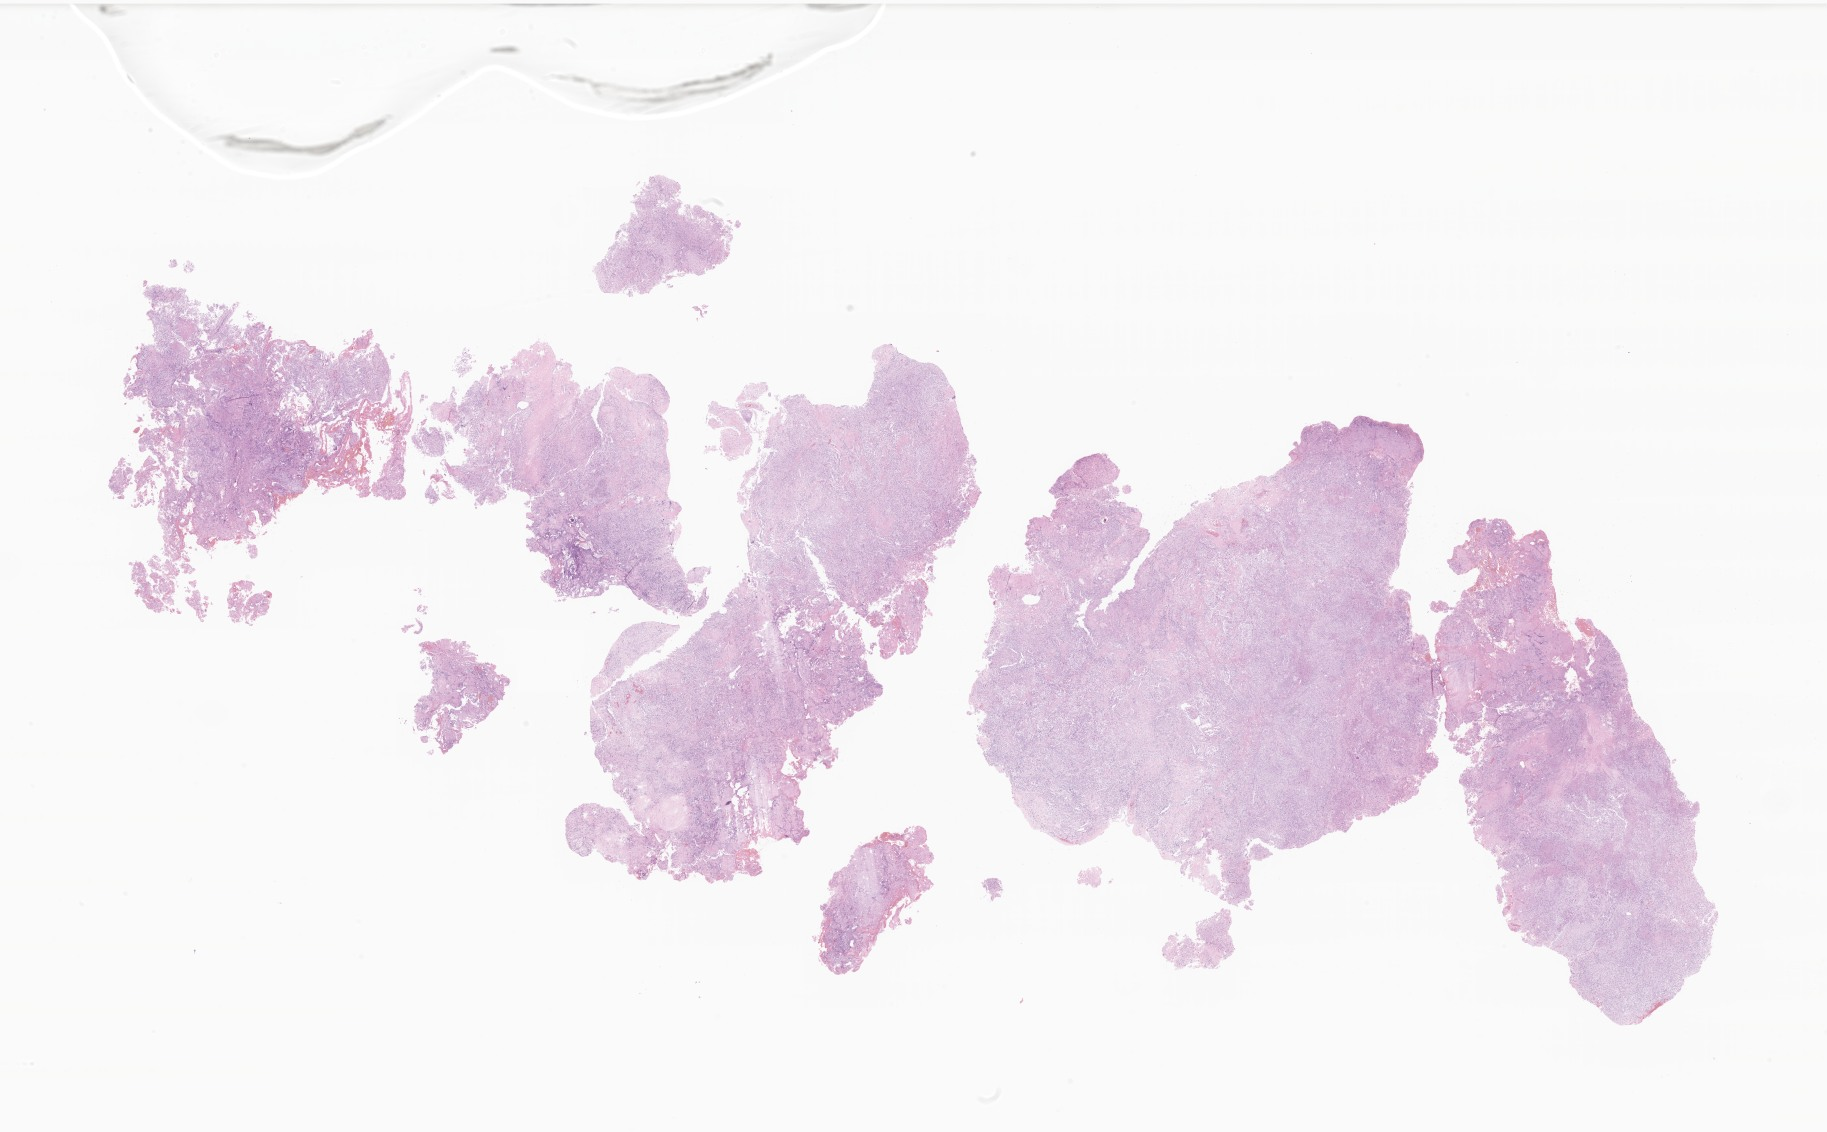
Whole-slide image, hematoxylin and eosin (H&E) stain of tumor tissue from the brain — low-resolution overview of the scanned area, about 30.8 x 19.1 mm, FFPE section. Patient male; age 108 months.
• diagnosis (ICD-O-3 morphology term): Meningioma, NOS